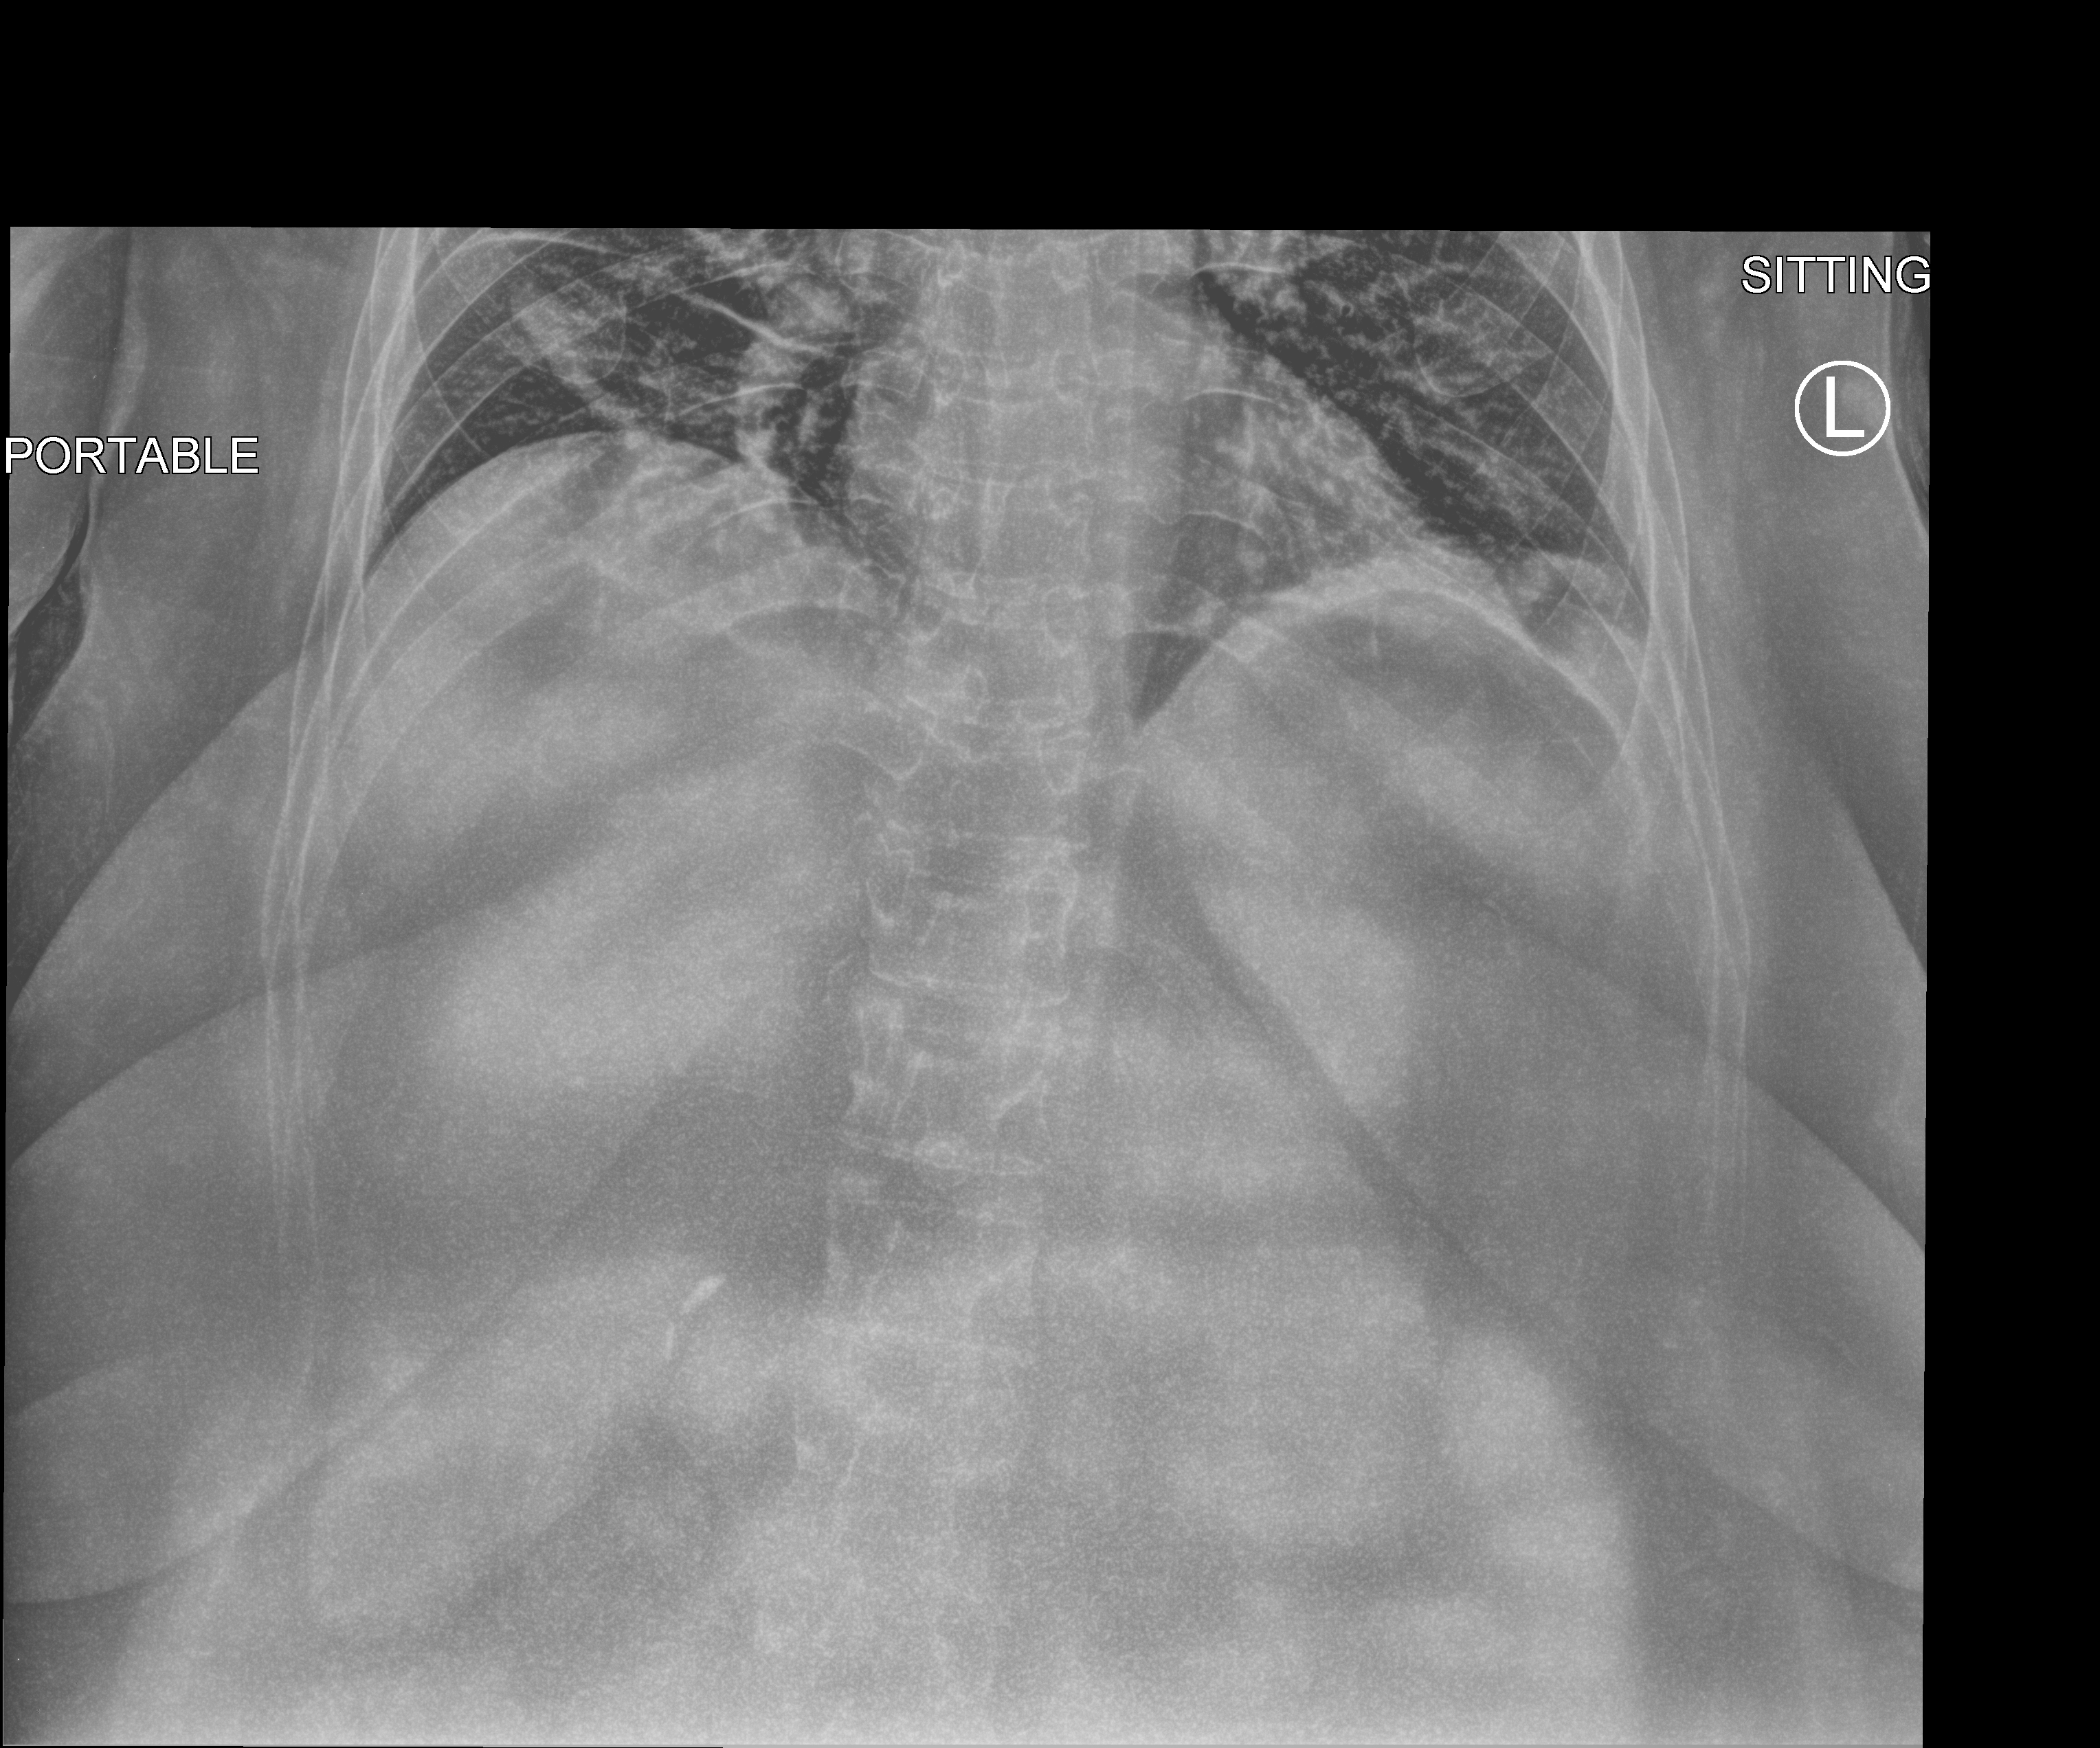
Abdomen X-ray (portable), anteroposterior (AP) projection. Female patient hospitalised with COVID-19, age 18–59 years.
Admission-level facts for this patient (not findings on this image; timing relative to this image not recorded):
- mechanically ventilated during this hospital stay: no